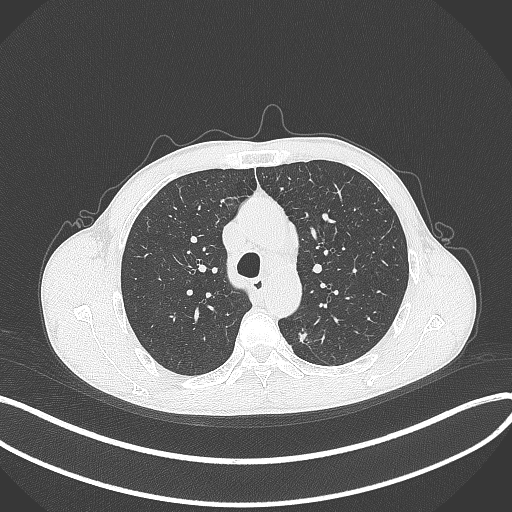
Chest CT, one axial slice; slice 278 of 429 in the series (ordered by position); 120 kVp; lung window (W 1500 / L -600 HU); 512 × 512 image matrix. Patient: male, 51 years. From the clinical record (not read from this slice): clinical TNM (as recorded): T2a N1 M1.
Outlined on this slice (rectangle marked by the reading radiologist):
- lung tumour (recorded histology: adenocarcinoma): box from (x=296, y=324) to (x=316, y=346) px